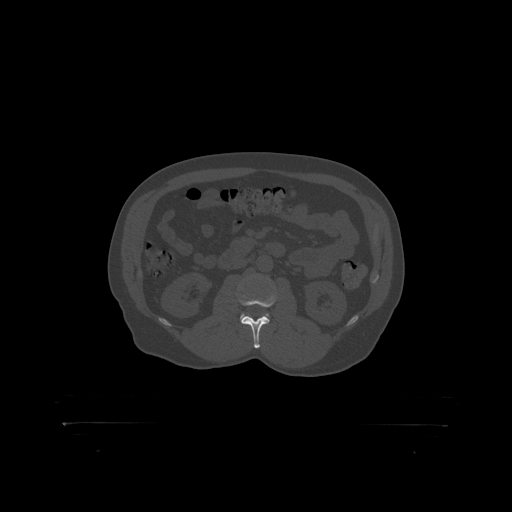
CT including the spine, one axial slice. Slice 286 of 399 in the series (ordered by position). Reconstruction kernel STANDARD. Bone window (W 1800 / L 400 HU). 512 × 512 image matrix, field of view 650 × 650 mm. Male patient, age 46 years. Case-level facts recorded for this patient, not image findings: primary cancer: skin.
Structures marked on this image (semi-automatically segmented with operator editing):
- L2 vertebra: bounding box [x1, y1, x2, y2] px = [239, 295, 277, 319]
- L3 vertebra: [241, 313, 270, 318]